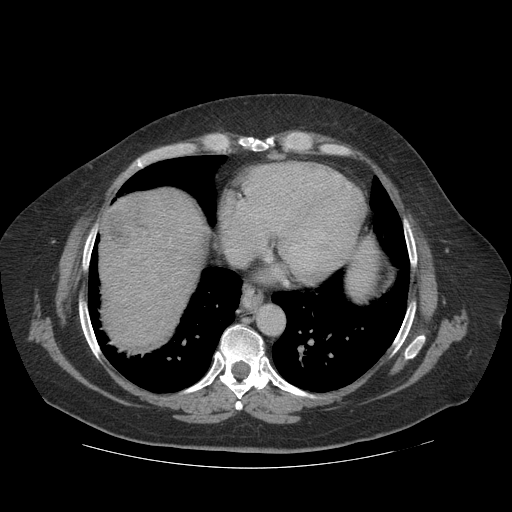
Contrast-enhanced abdominal CT (liver protocol), one axial slice. Slice 105 of 121 in the series (ordered by position). Reconstruction kernel STANDARD. 140 kVp. Soft-tissue window (W 400 / L 40 HU). 2.5 mm slice thickness. 512 × 512 image matrix, field of view 420 × 420 mm. Case-level facts recorded for this patient, not image findings: diagnosis: hepatocellular carcinoma (patient treated with transarterial chemoembolisation; whether this scan precedes or follows treatment is not stated here); TNM stage (as recorded): Stage-IIIA; Child-Pugh class: A; tumour differentiation: well differentiated; tumour nodularity: multinodular.
Outlined on this slice (semi-automatic segmentation, software-assisted and operator-edited):
- liver parenchyma outside the tumour (the mass and vessels are separate outlines, so this box may not span the whole liver): bounding box <98,188,204,346> (left, top, right, bottom; pixels)
- mass: <97,194,150,248>